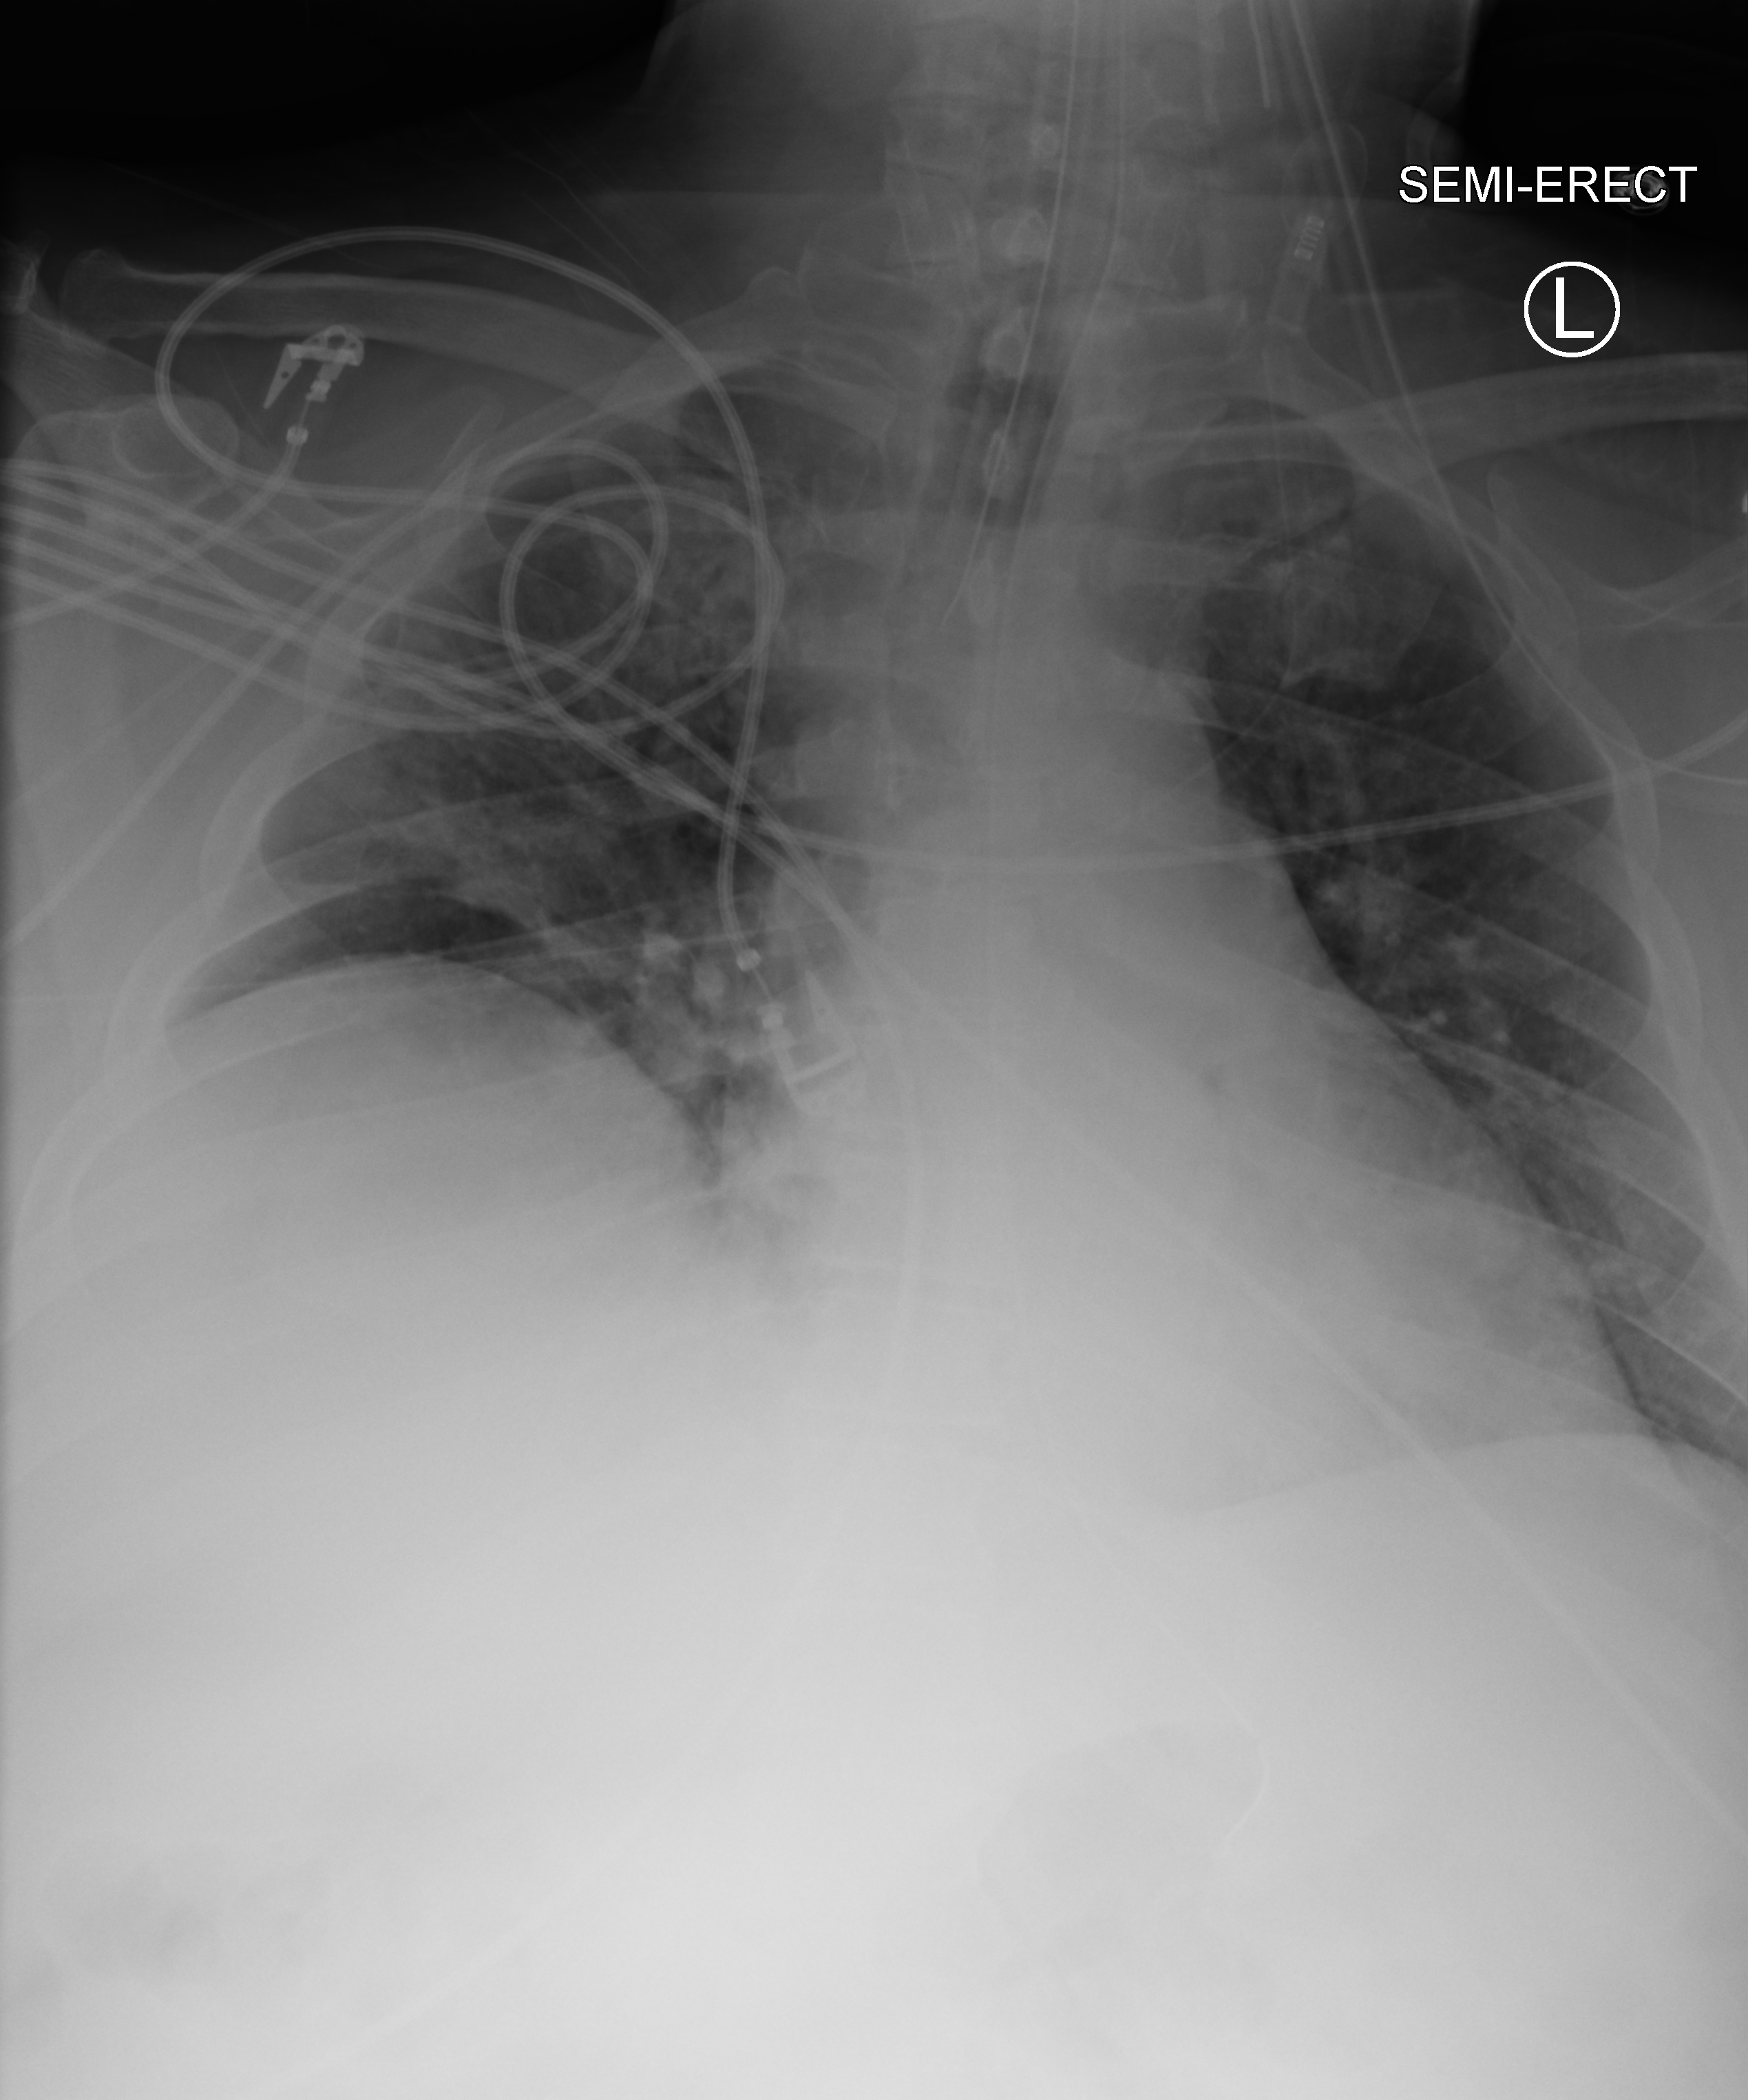
Chest X-ray (portable), anteroposterior (AP) projection. Male patient hospitalised with COVID-19, age 18–59 years.
Hospital-stay facts (about this admission, not read from this image; timing relative to this image not recorded): admitted to intensive care during this hospital stay: yes; mechanically ventilated during this hospital stay: yes.